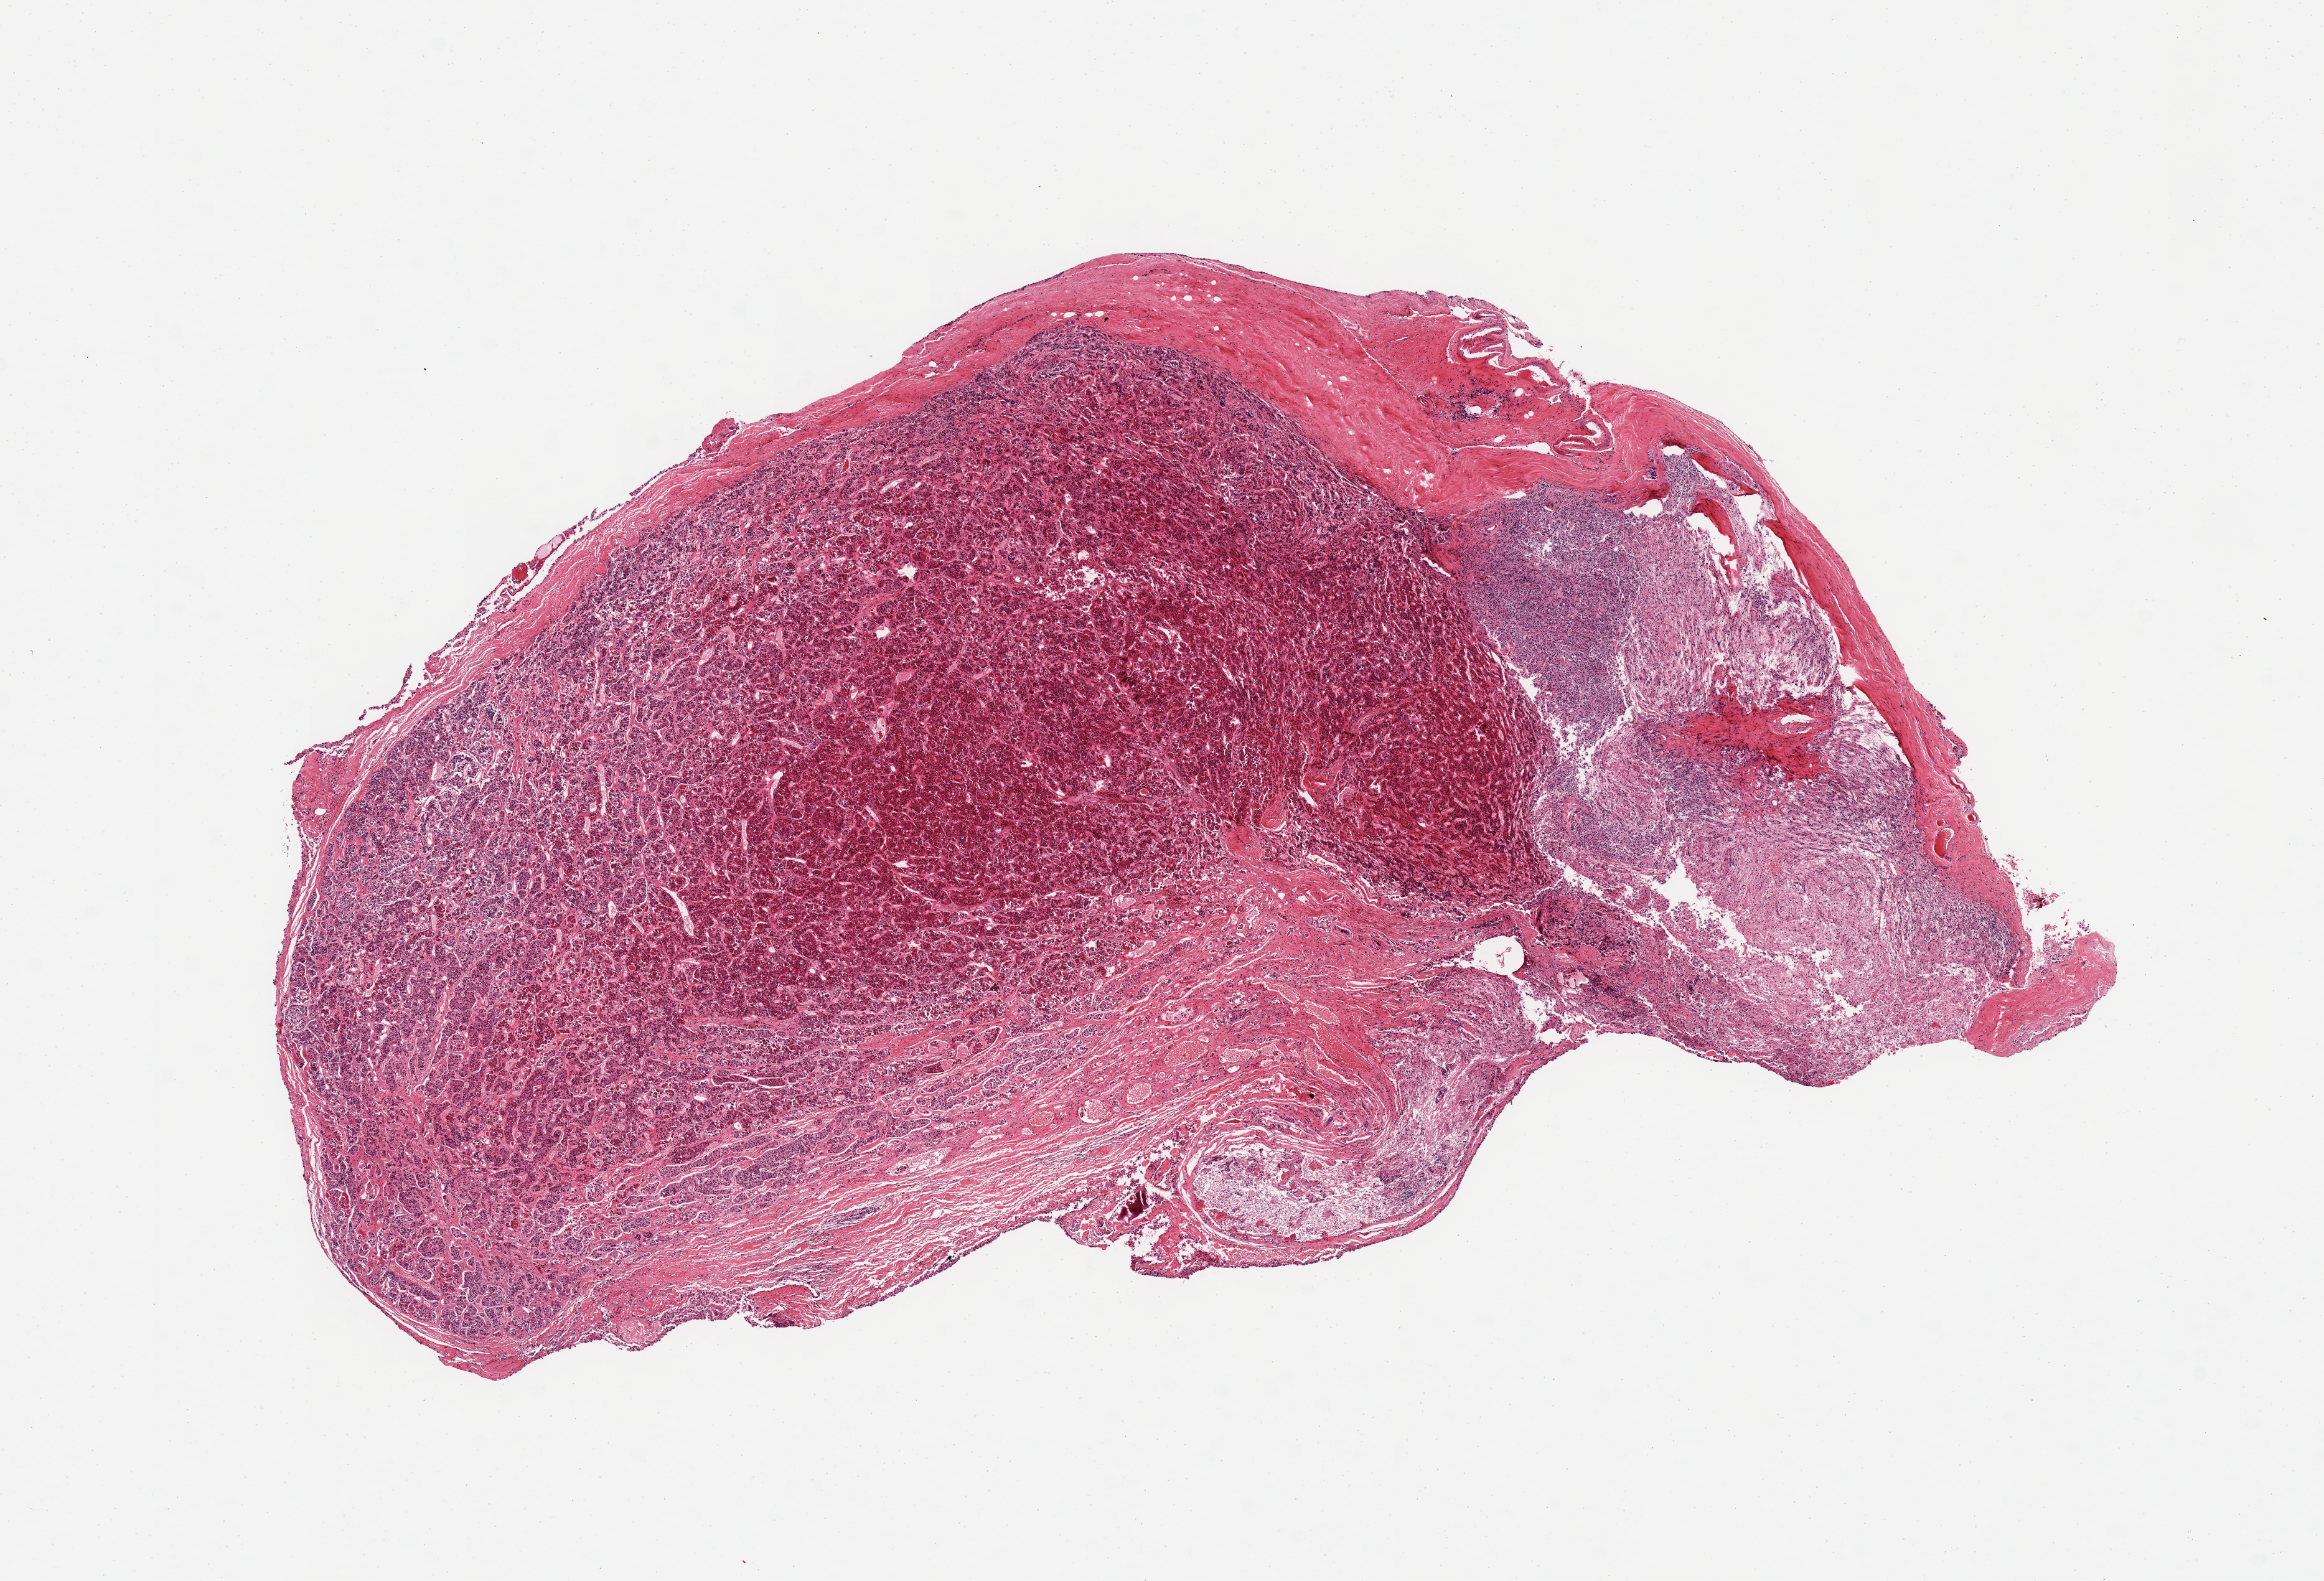
Whole-slide image, haematoxylin and eosin stain — low-resolution overview of the scanned area, about 14.8 x 10.0 mm, PAXgene-fixed, paraffin-embedded tissue, target tissue: pituitary, tissue donor sample. Donor sex: female.
Reviewer comment on this tissue sample: 1 piece; mostly adenohypophysis; neural portion marked.